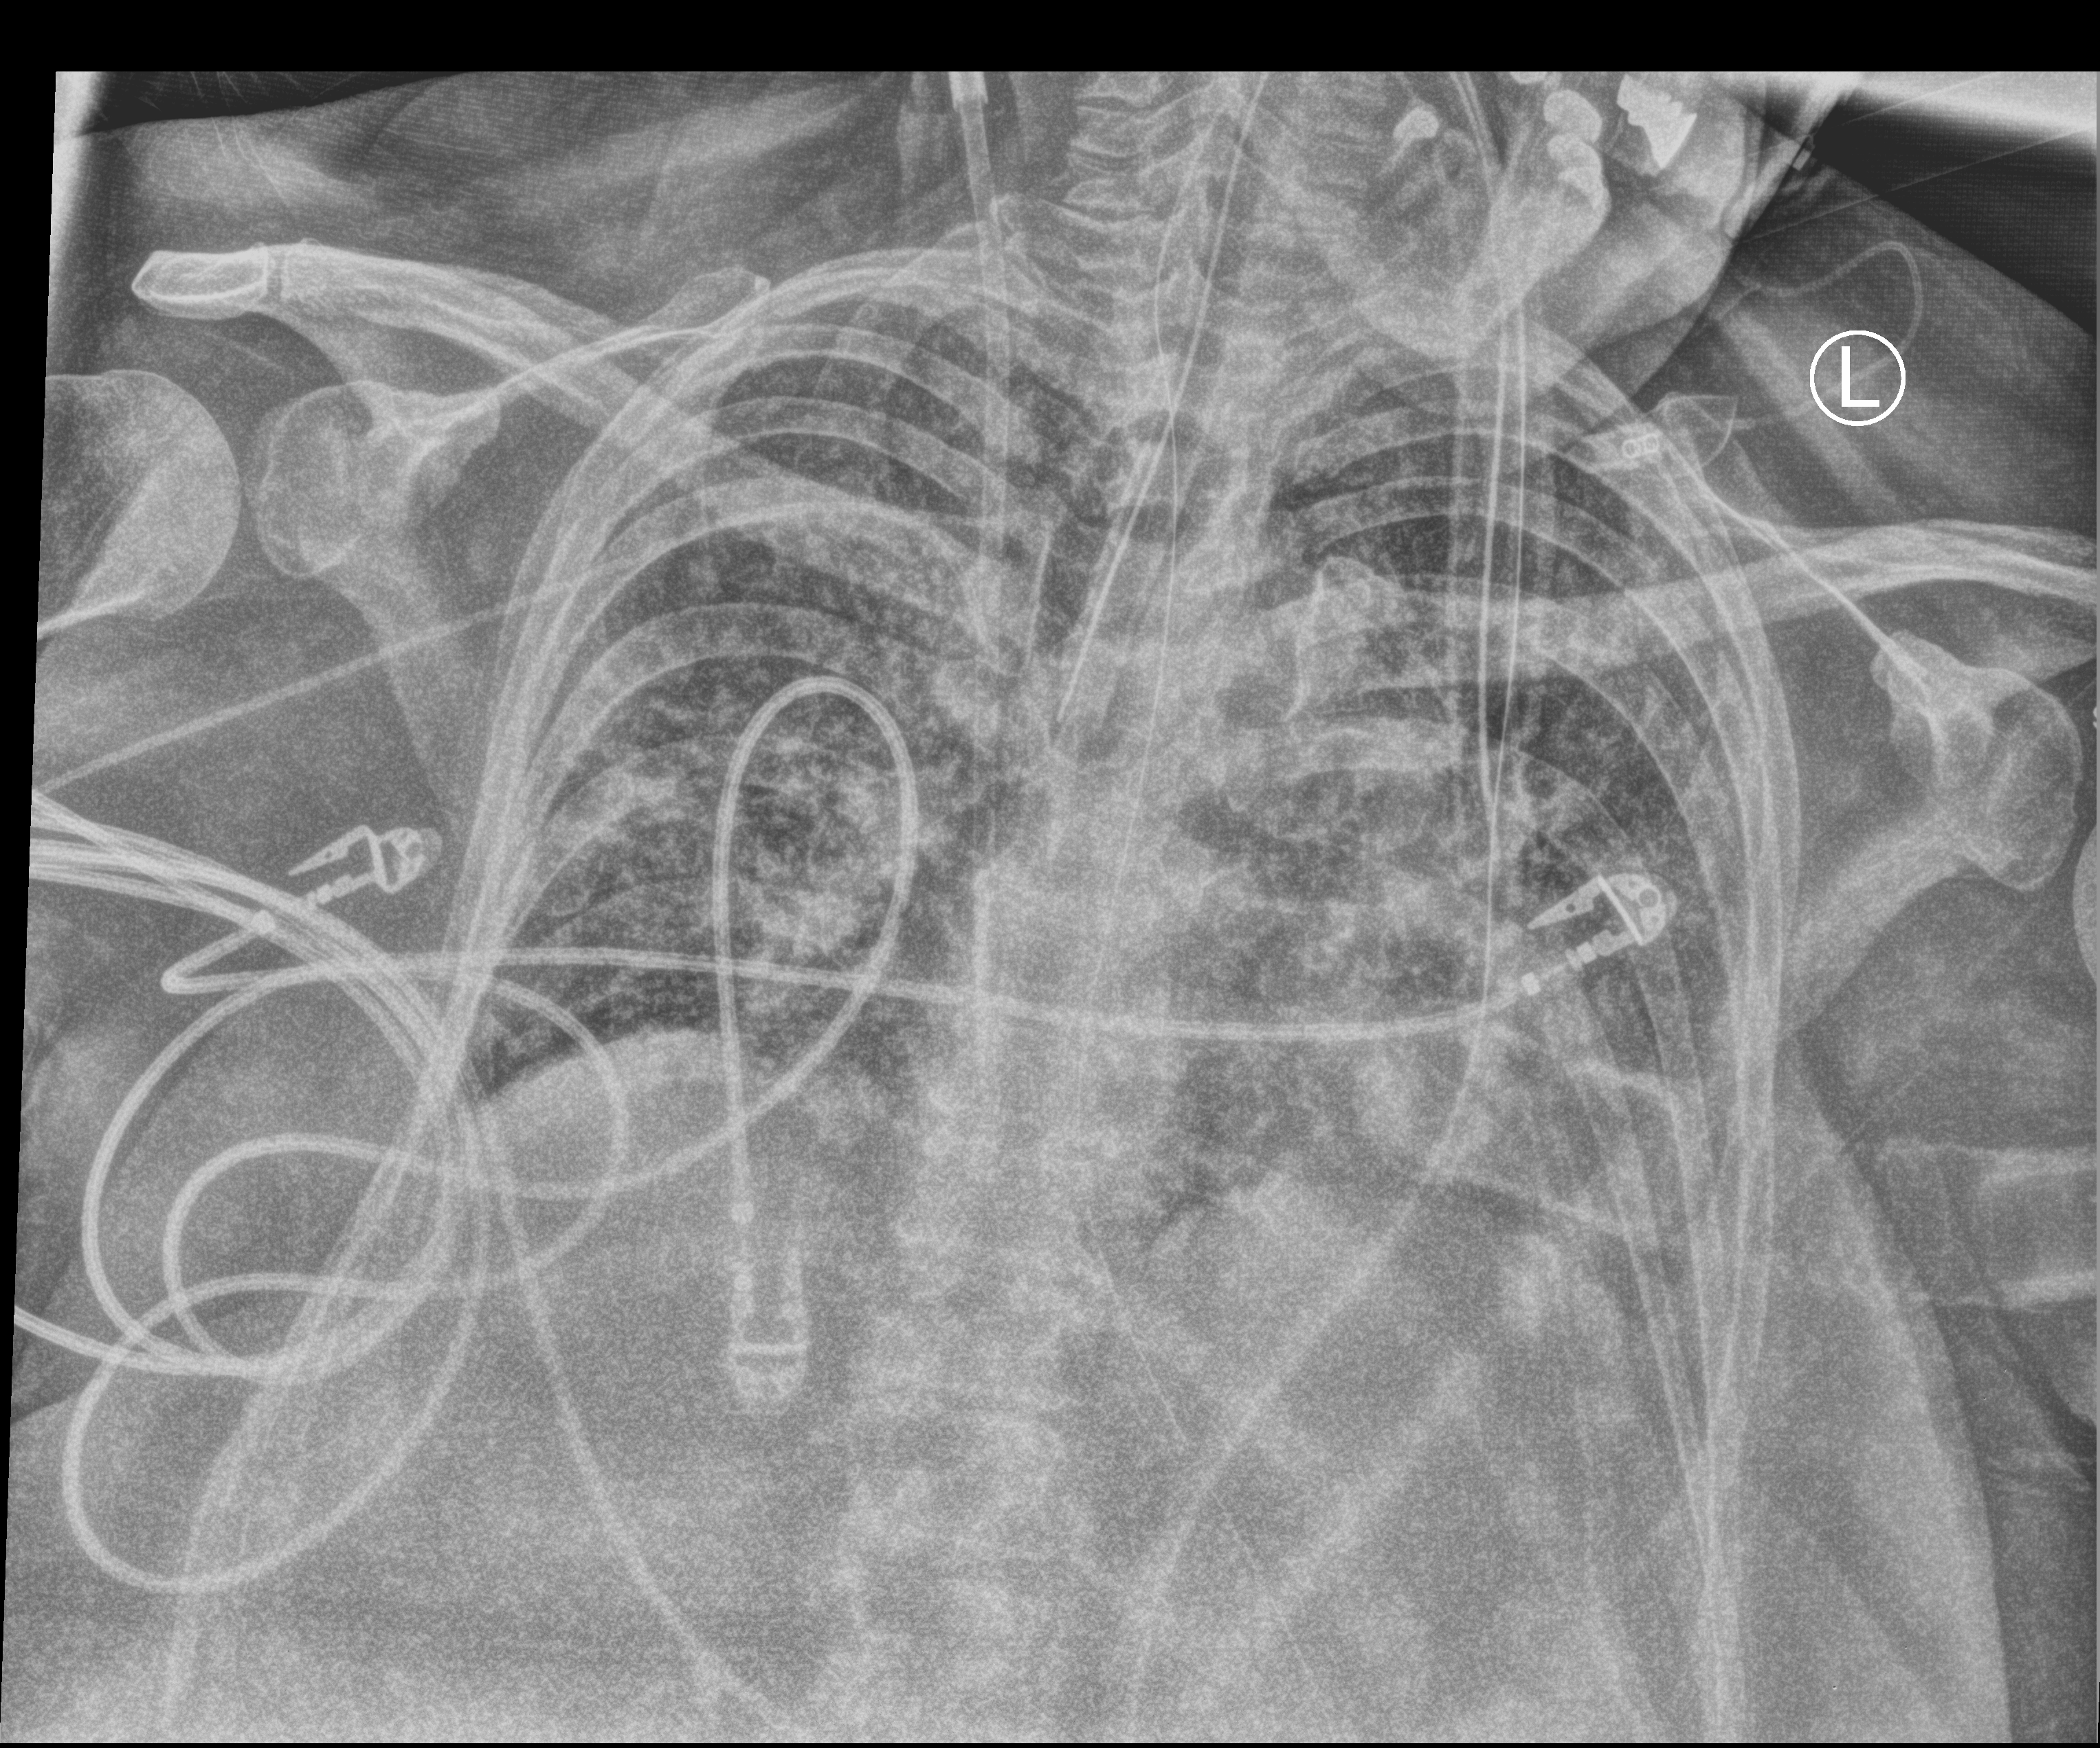
Chest X-ray (portable); anteroposterior (AP) projection. Female patient hospitalised with COVID-19, age 60–74 years.
From the hospital-stay record, not from the radiograph (when in the stay this image was taken is not recorded):
- admitted to intensive care during this hospital stay: yes
- COPD (admission record): no